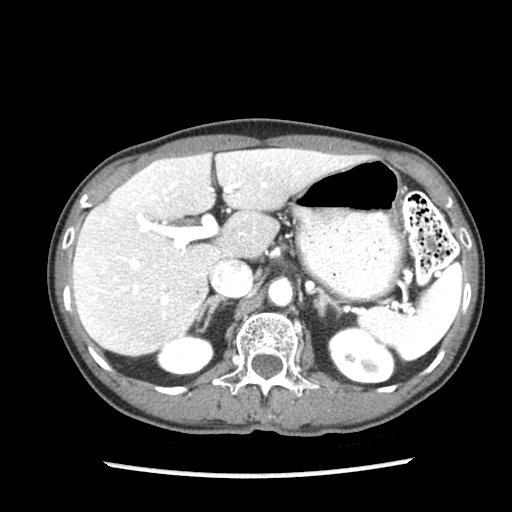
Contrast-enhanced abdominal CT (liver protocol), one axial slice. Soft-tissue window (W 400 / L 40 HU). 512 × 512 image matrix, field of view 300 × 300 mm. From the clinical record (not read from this slice): diagnosis: hepatocellular carcinoma (patient treated with transarterial chemoembolisation; whether this scan precedes or follows treatment is not stated here); TNM stage (as recorded): Stage-IIIB; Child-Pugh class: A; tumour nodularity: uninodular.
Structures marked on this image (semi-automatically segmented with operator editing):
- liver parenchyma outside the tumour (the mass and vessels are separate outlines, so this box may not span the whole liver): bounding box [x1, y1, x2, y2] px = [72, 148, 360, 356]
- liver vessels: [91, 162, 271, 316]